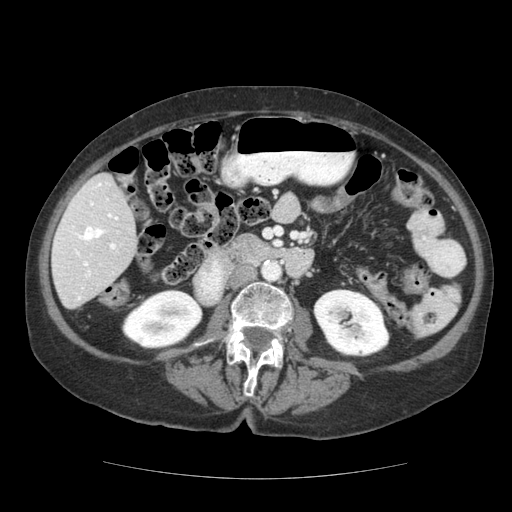
Contrast-enhanced abdominal CT (liver protocol), one axial slice; slice 48 of 111 in the series (ordered by position); reconstruction kernel STANDARD; 140 kVp; soft-tissue window (W 400 / L 40 HU); 2.5 mm slice thickness; 512 × 512 image matrix, field of view 360 × 360 mm. Case-level facts recorded for this patient, not image findings: diagnosis: hepatocellular carcinoma (patient treated with transarterial chemoembolisation; whether this scan precedes or follows treatment is not stated here); TNM stage (as recorded): Stage-I; Child-Pugh class: A; tumour differentiation: moderately-poorly differentiated; tumour nodularity: uninodular.
Annotated regions visible in this slice (semi-automatically segmented with operator editing):
- liver parenchyma outside the tumour (the mass and vessels are separate outlines, so this box may not span the whole liver): bounding box <52,174,136,308> (left, top, right, bottom; pixels)
- liver vessels: <55,183,118,300>